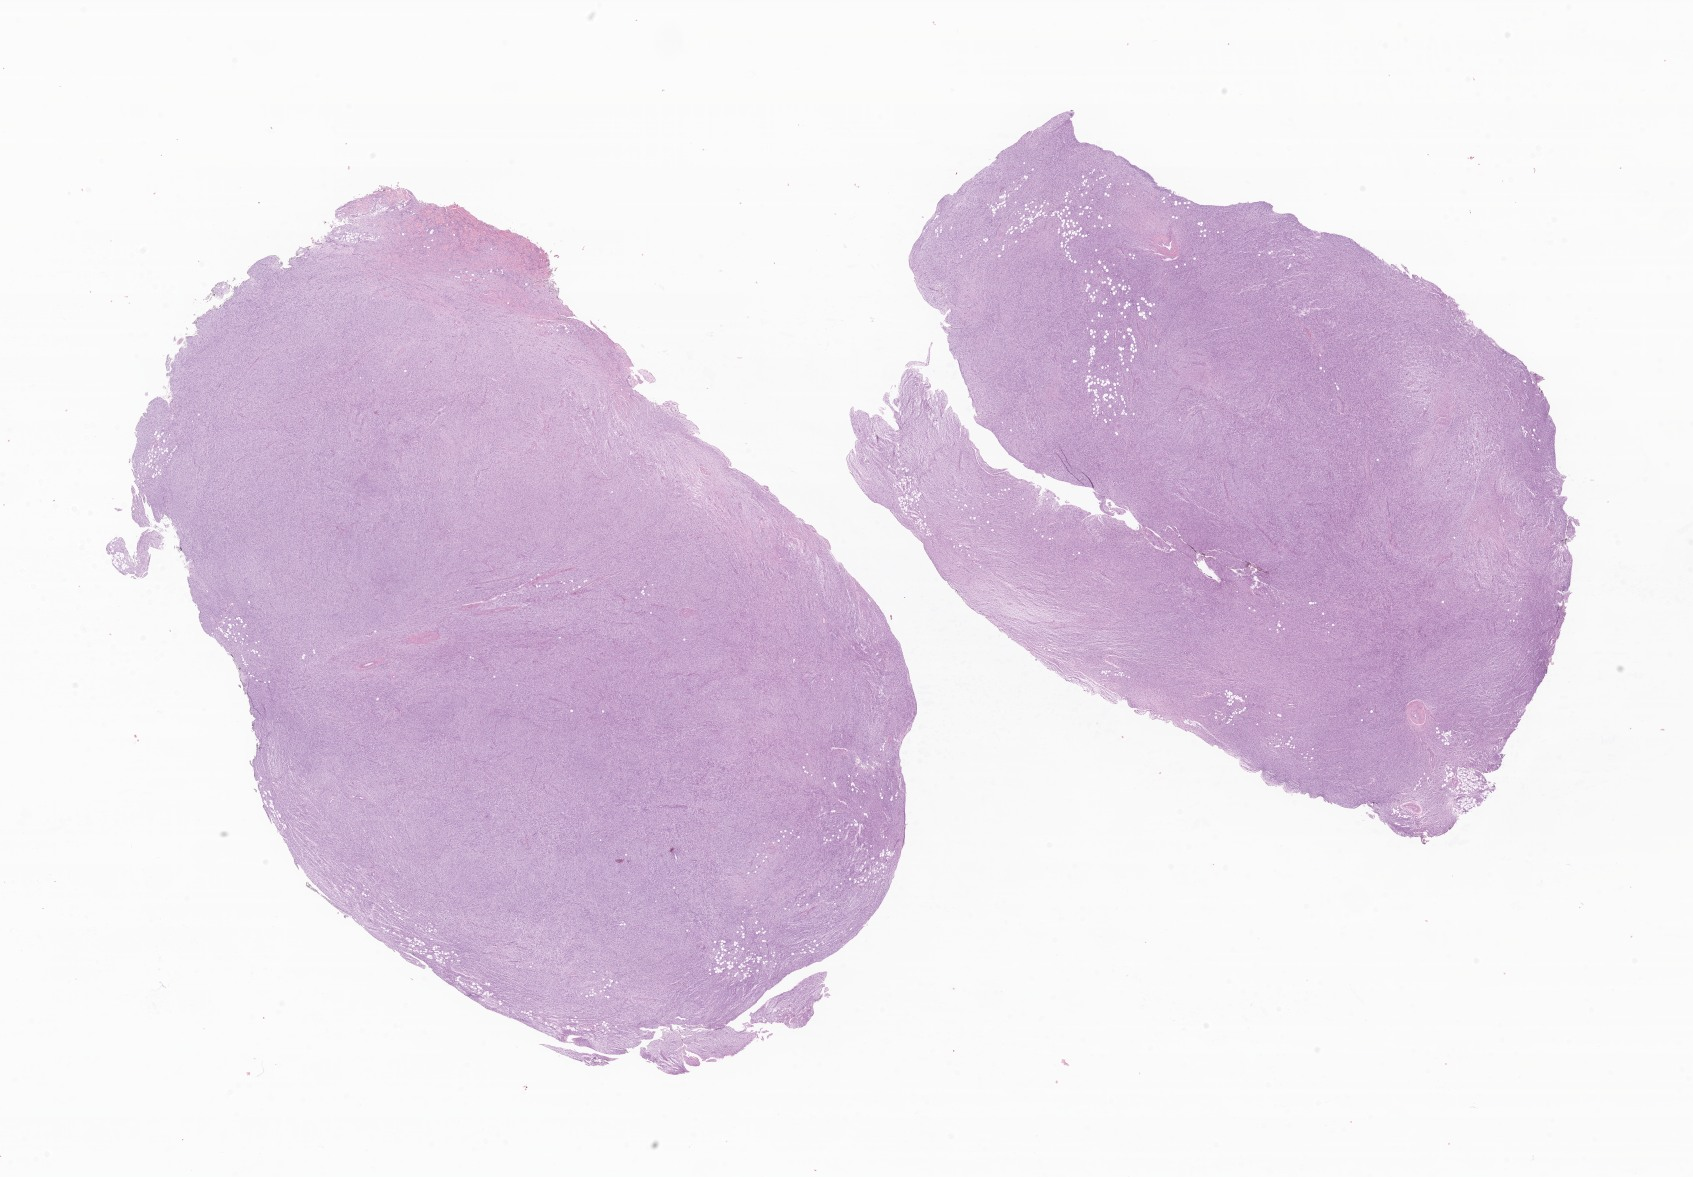
Whole-slide image, haematoxylin and eosin stain of tumor tissue from the lower limb, whole scanned area (about 28.6 x 19.9 mm) shown as a low-resolution overview, formalin-fixed, paraffin-embedded (FFPE) tissue. Patient male; age 40 months (3 years 4 months).
Diagnosis (ICD-O-3 morphology term): Spindle cell sarcoma.